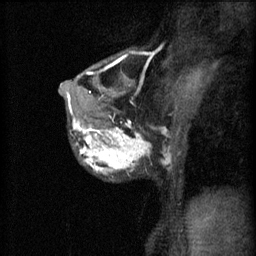
Breast MRI (dynamic contrast-enhanced), one sagittal slice. Slice 39 of 60 in the series (ordered by position). 3 images stored at this slice position (order not interpretable as contrast timing). 1.5 T. TE 4.2 ms, TR 11 ms. 256 × 256 image matrix. Female patient, age 37 years.
Structures marked on this image (semi-automatically segmented with operator editing):
- analysis volume of interest (the breast-tissue region the enhancement analysis was run in; not a lesion): bounding box (x1, y1, x2, y2) in pixels: (68, 118, 174, 181)
- tumour enhancement mask (voxels above the 70 % enhancement threshold inside the analysis volume of interest): (73, 118, 170, 173)